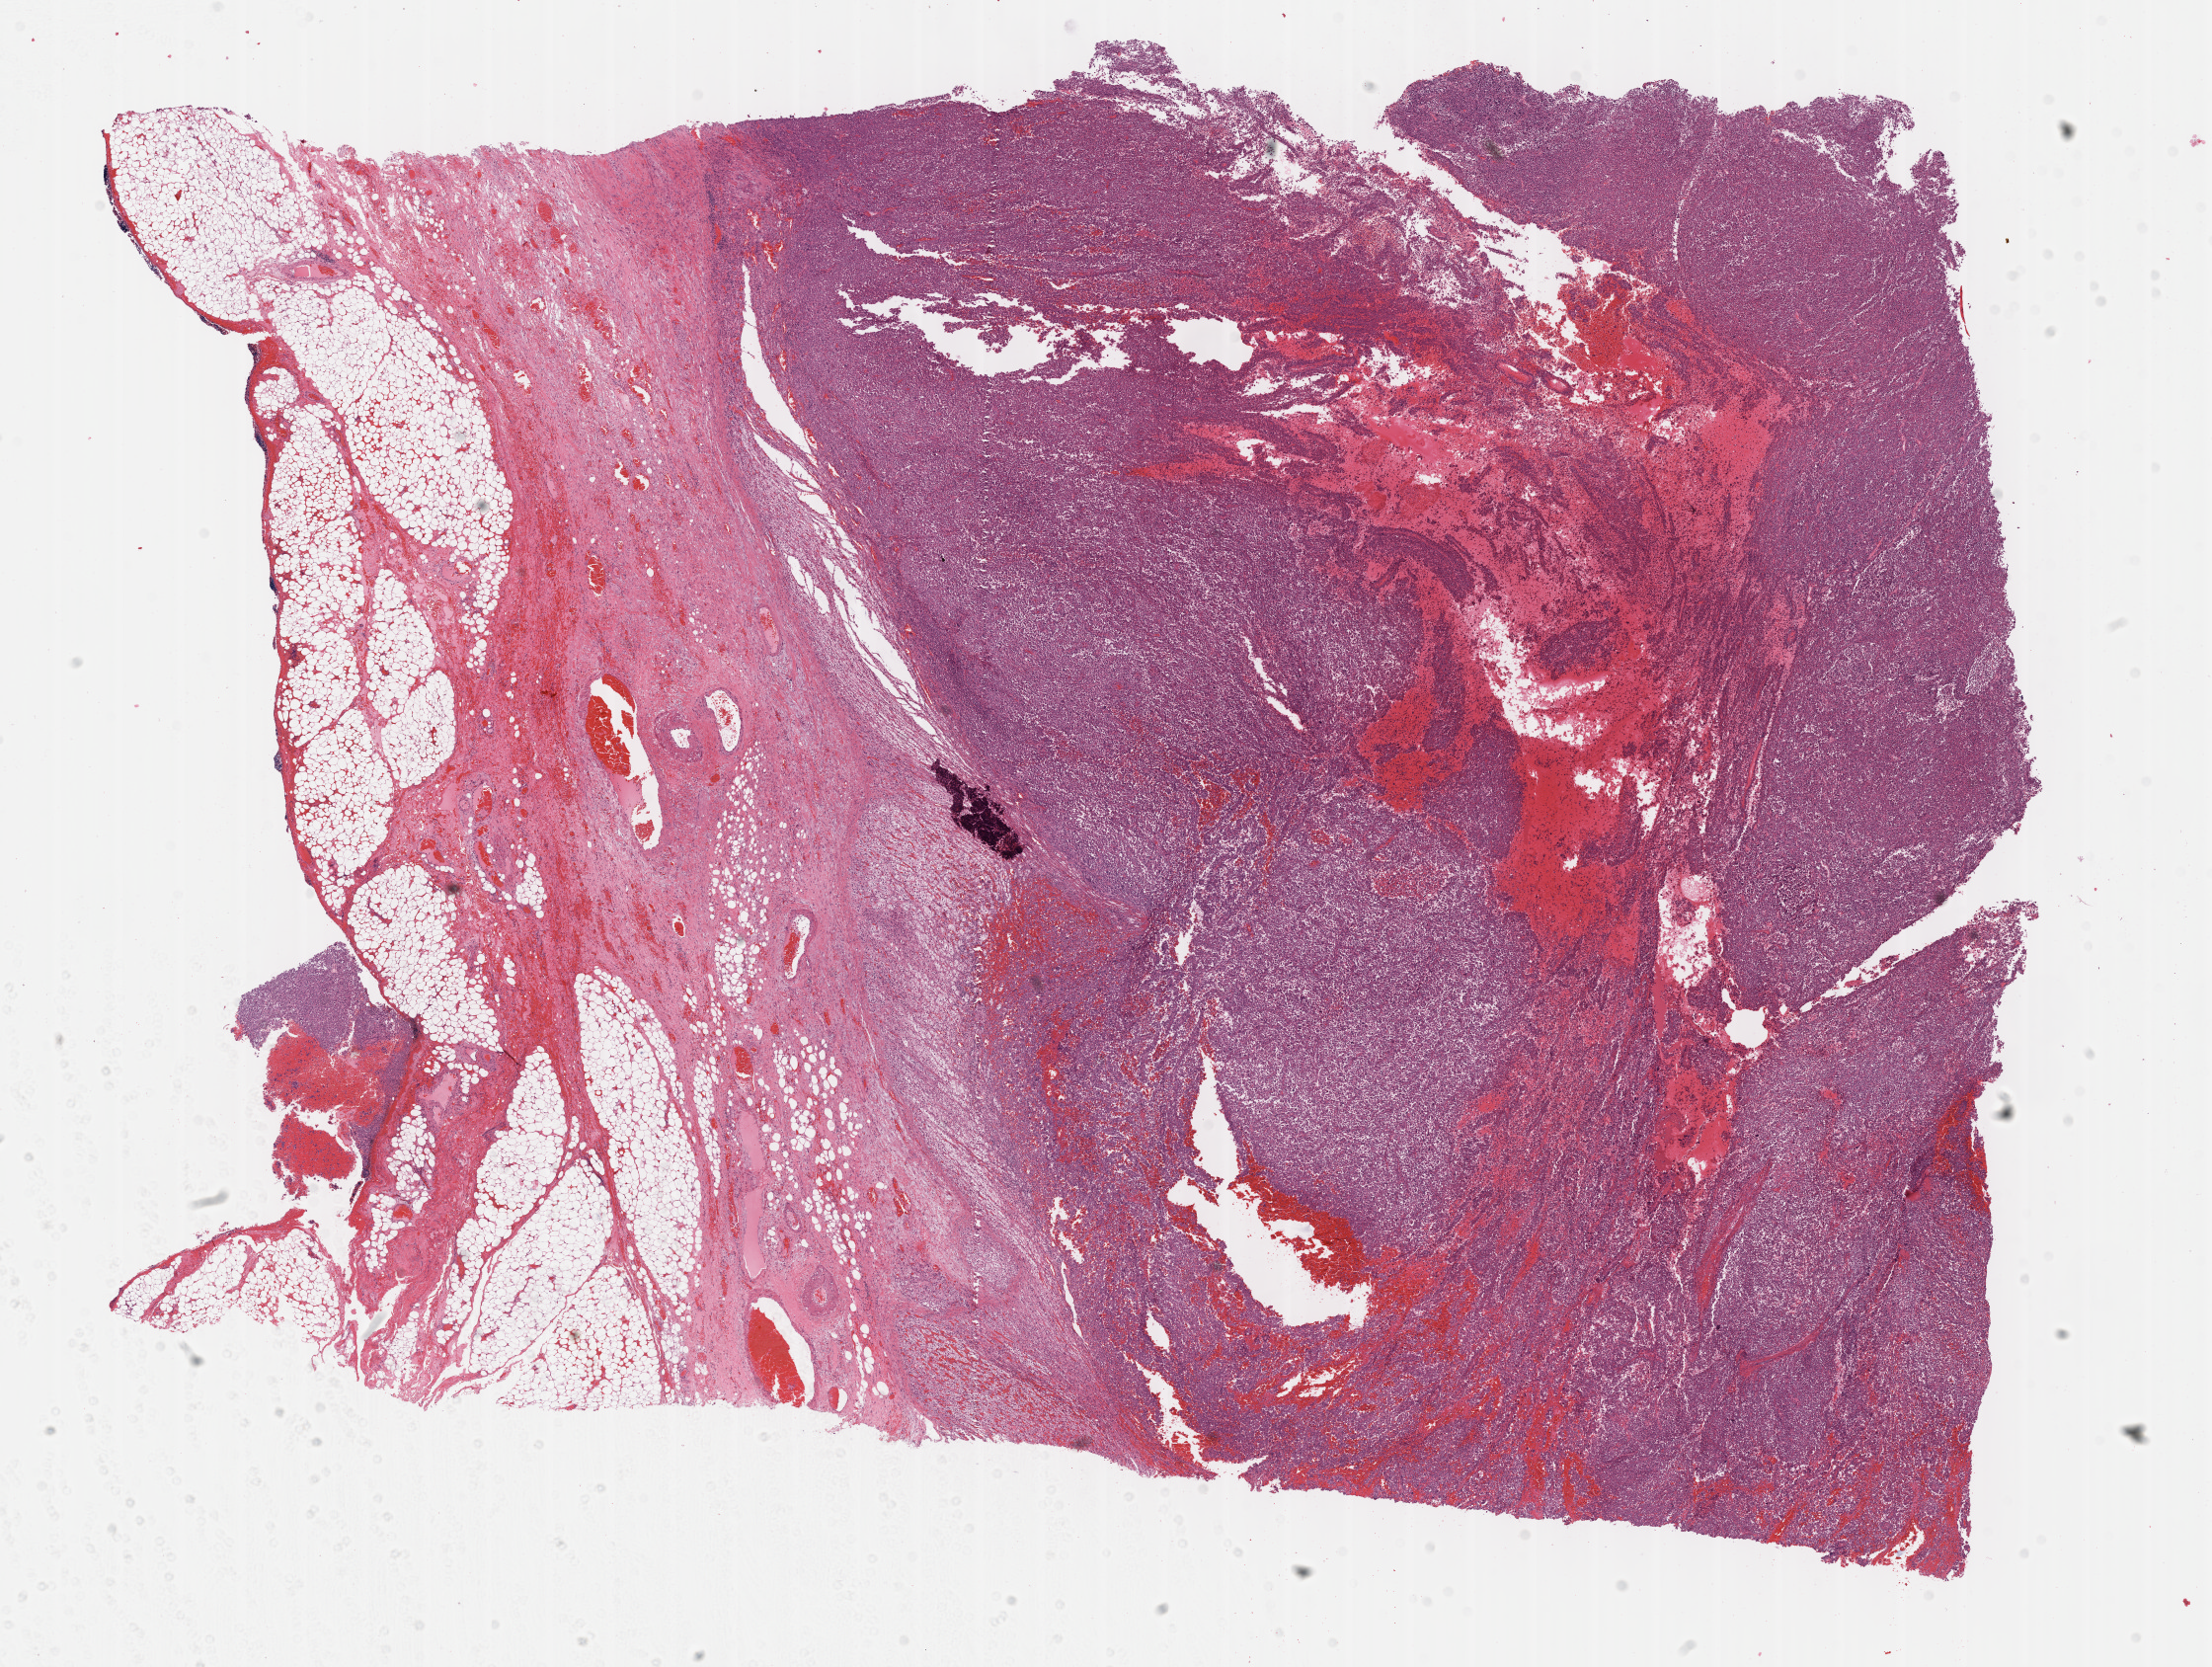
Whole-slide histology image, H&E — whole scanned area (about 18.1 x 13.7 mm, from a 40x scan) shown as a low-resolution overview. Formalin-fixed paraffin-embedded (FFPE) diagnostic section. Adrenal cortex, primary tumour sample. Male patient; age at initial diagnosis 52 years.
Histologic diagnosis: Adrenal cortical carcinoma (cortex of adrenal gland).